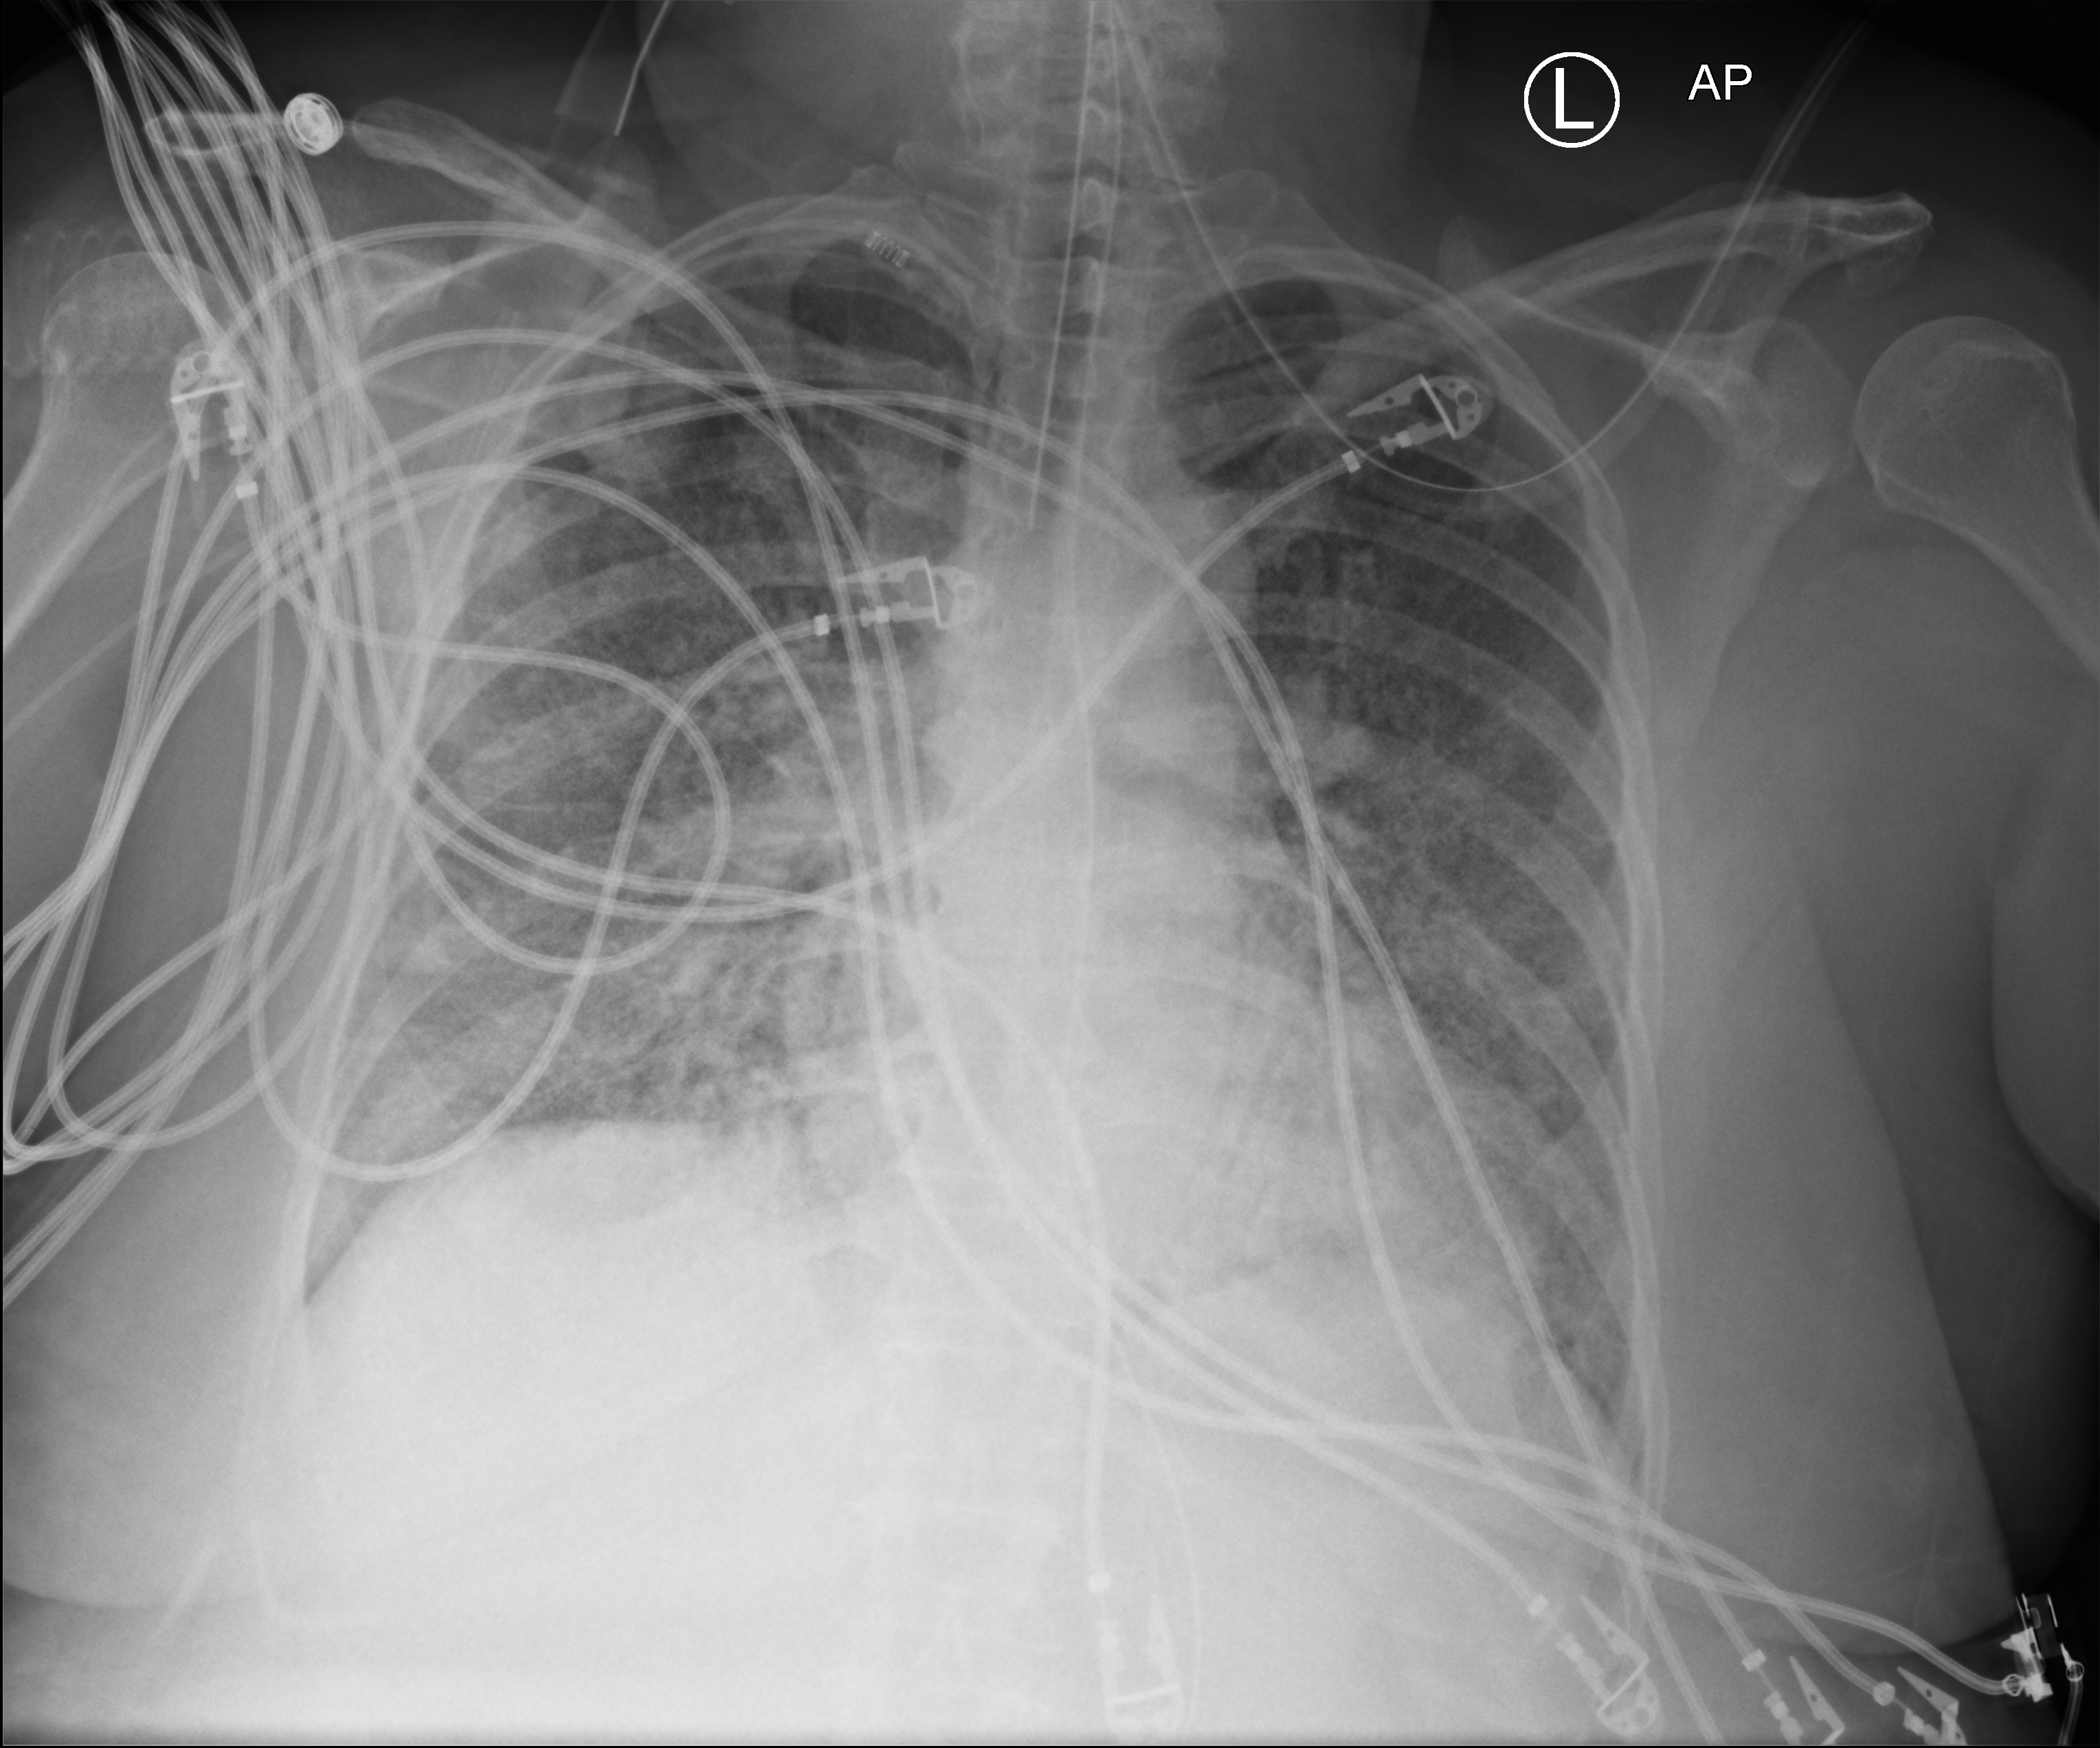
Chest X-ray (portable); anteroposterior (AP) projection. Female patient hospitalised with COVID-19, age 60–74 years.
Admission-level facts for this patient (not findings on this image; timing relative to this image not recorded): admitted to intensive care during this hospital stay: yes; other chronic lung disease (admission record): no; length of hospital stay: 38 days.